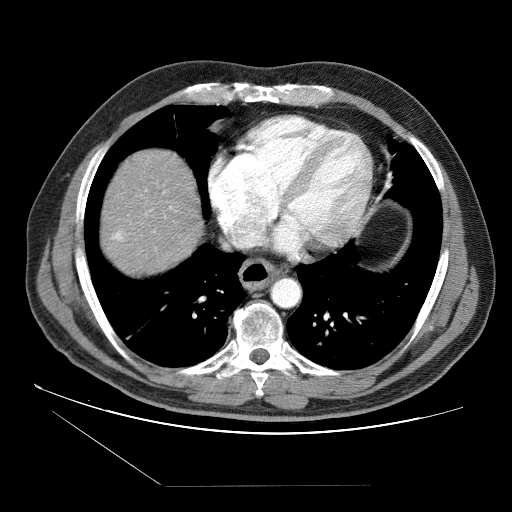
Contrast-enhanced abdominal CT (liver protocol), one axial slice. Position 79 of 87 along the scan axis. 120 kVp. Soft-tissue window (W 400 / L 40 HU). 2.5 mm slice thickness. 512 × 512 image matrix. From the clinical record (not read from this slice): diagnosis: hepatocellular carcinoma (patient treated with transarterial chemoembolisation; whether this scan precedes or follows treatment is not stated here); TNM stage (as recorded): Stage-II; Child-Pugh class: B; tumour differentiation: no biopsy; tumour nodularity: multinodular.
Outlined on this slice (semi-automatic segmentation, software-assisted and operator-edited):
- liver parenchyma outside the tumour (the mass and vessels are separate outlines, so this box may not span the whole liver): bounding box <102,150,202,272> (left, top, right, bottom; pixels)
- liver vessels: <113,232,122,240>